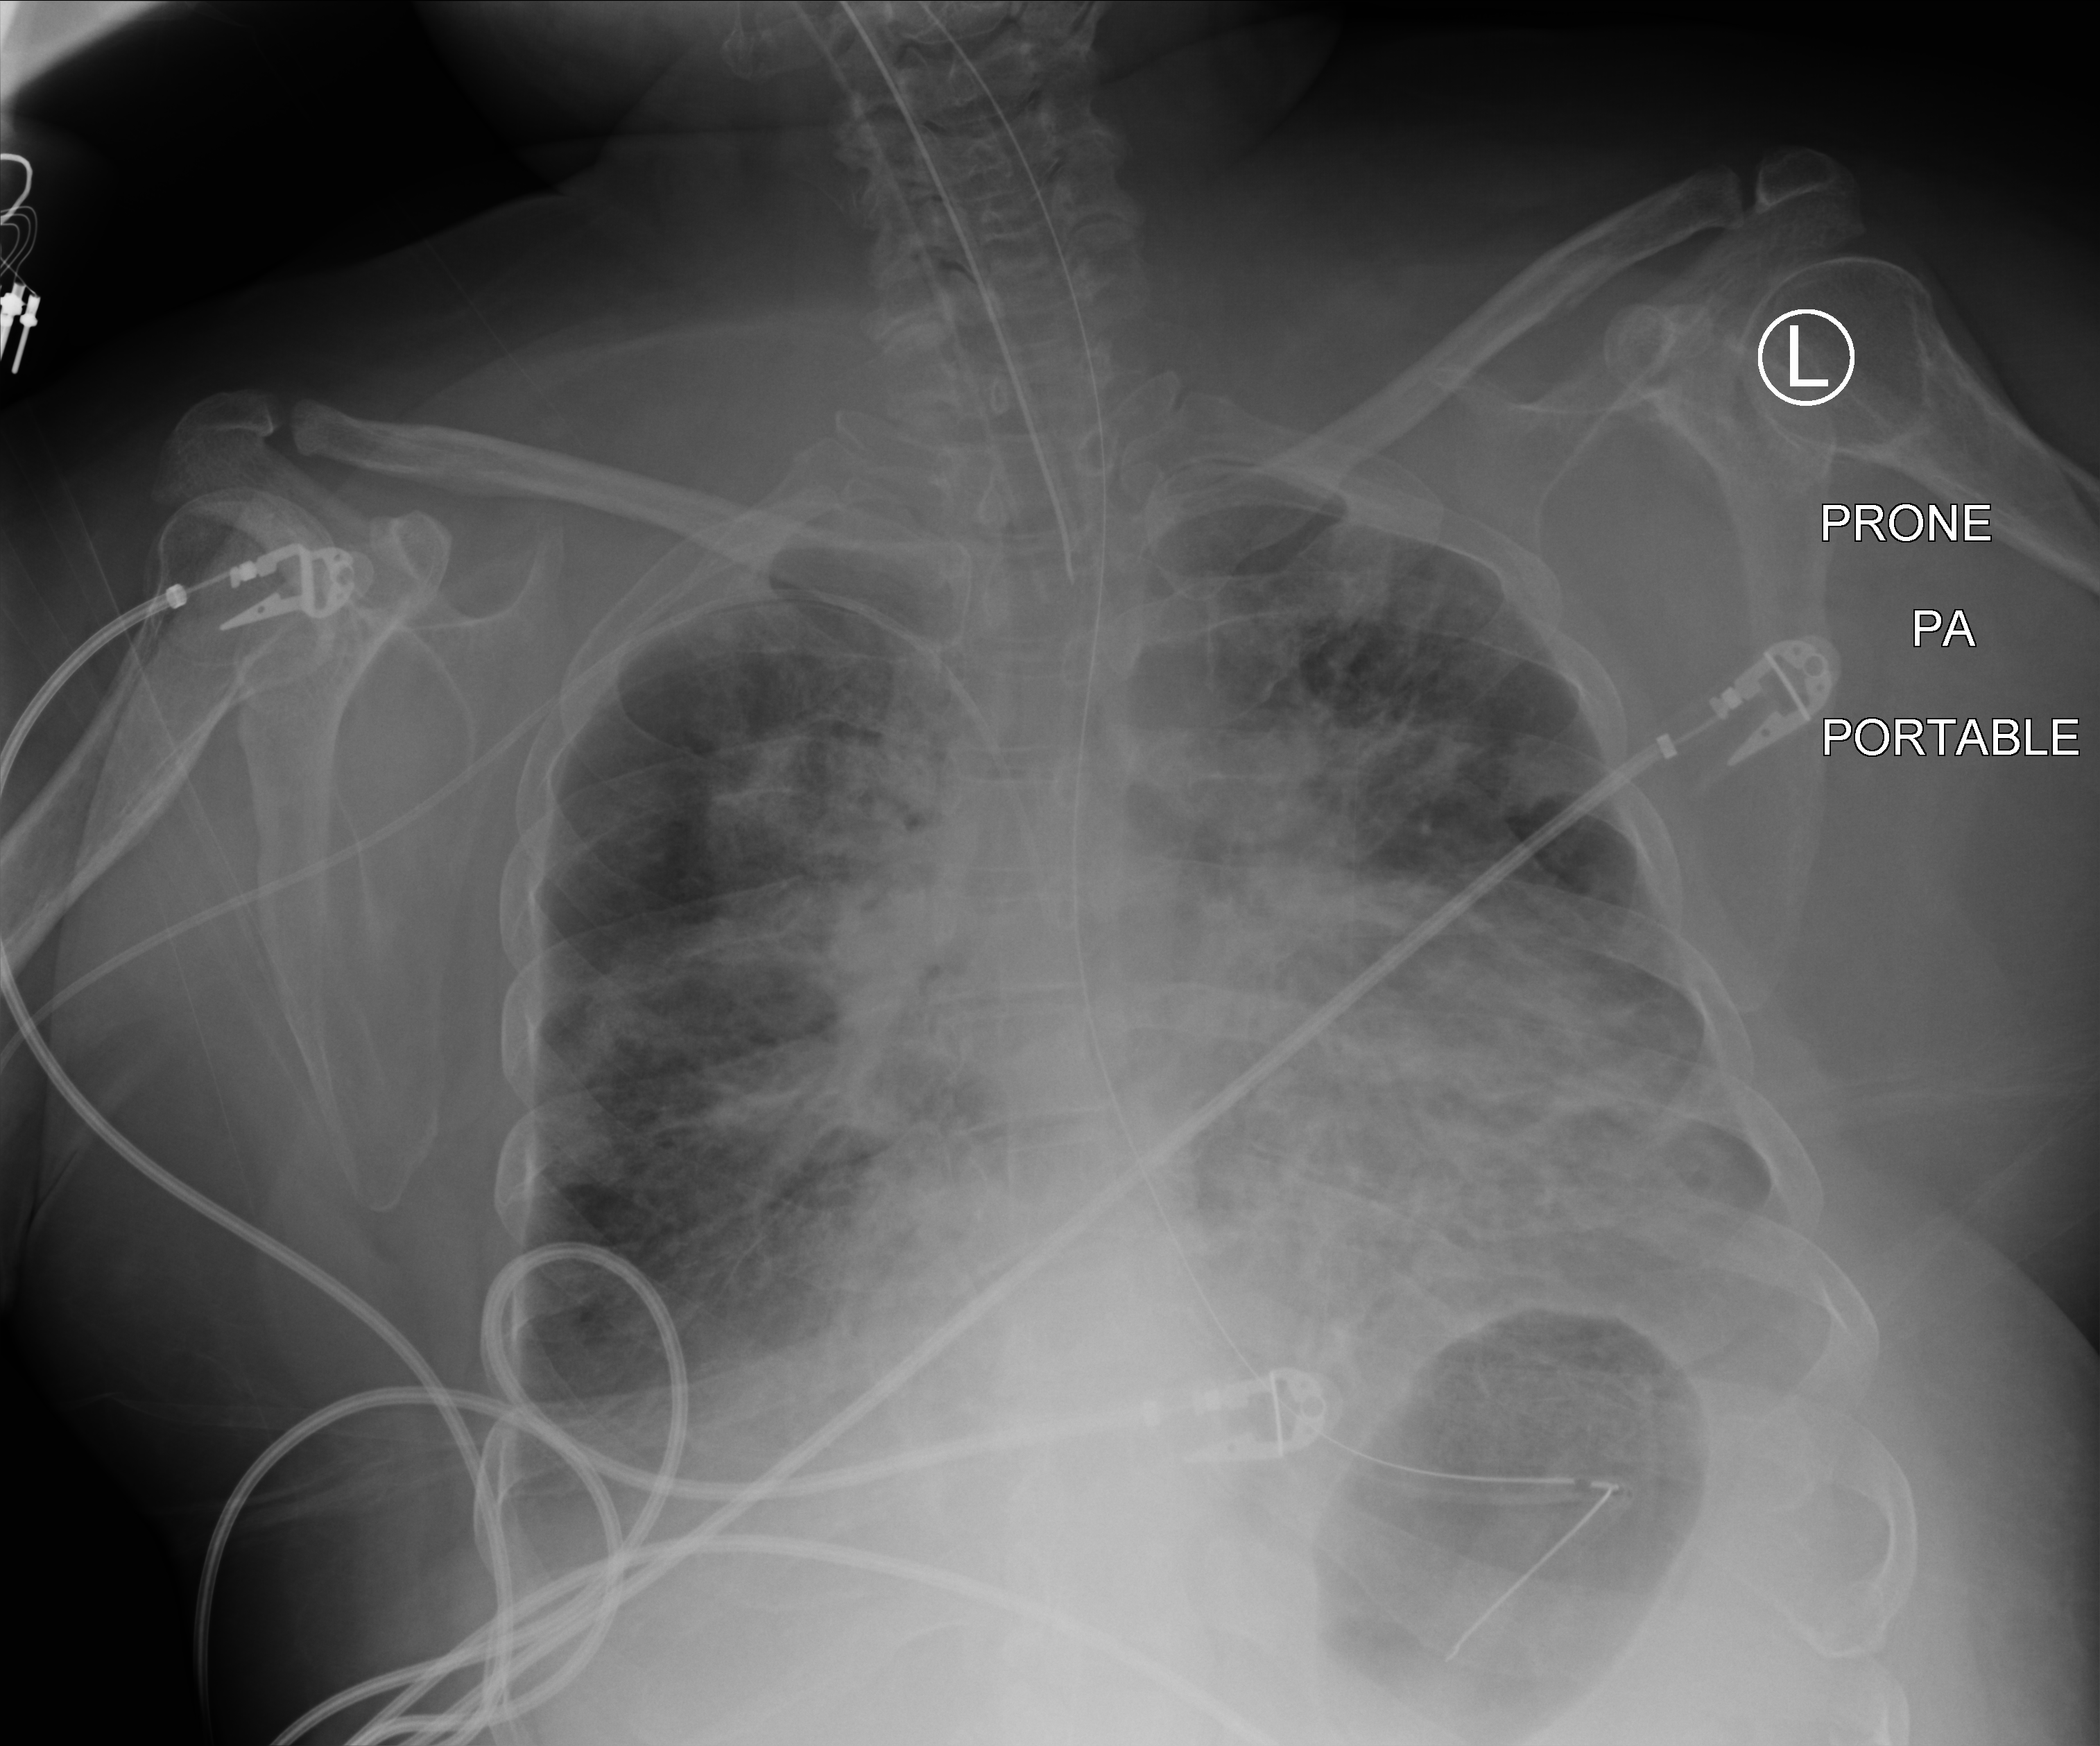
Portable chest radiograph, anteroposterior (AP) projection. Adult patient hospitalised with COVID-19, age 18–59 years.
From the hospital-stay record, not from the radiograph (when in the stay this image was taken is not recorded):
- length of hospital stay: 15 days
- mechanically ventilated during this hospital stay: yes
- admitted to intensive care during this hospital stay: yes